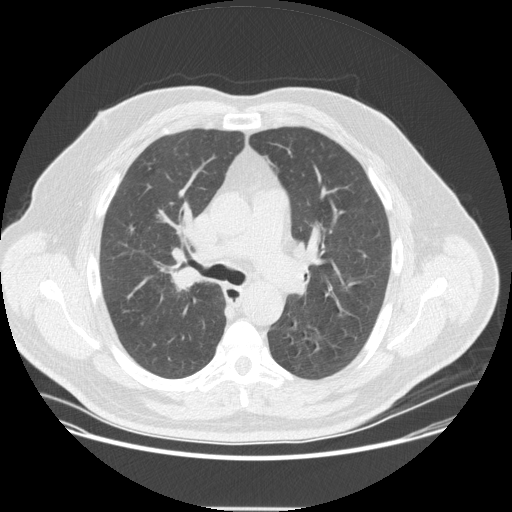
Low-dose screening chest CT, one axial slice. Slice 226 of 351 in the series (ordered by position). Reconstruction kernel STANDARD. 120 kVp. Lung window (W 1500 / L -600 HU). 512 × 512 image matrix, field of view 419 × 419 mm.
Annotated regions visible in this slice (expert manual segmentation):
- lesion 1 (tumor, upper lobe of right lung): bounding box <169,269,203,292> (left, top, right, bottom; pixels)